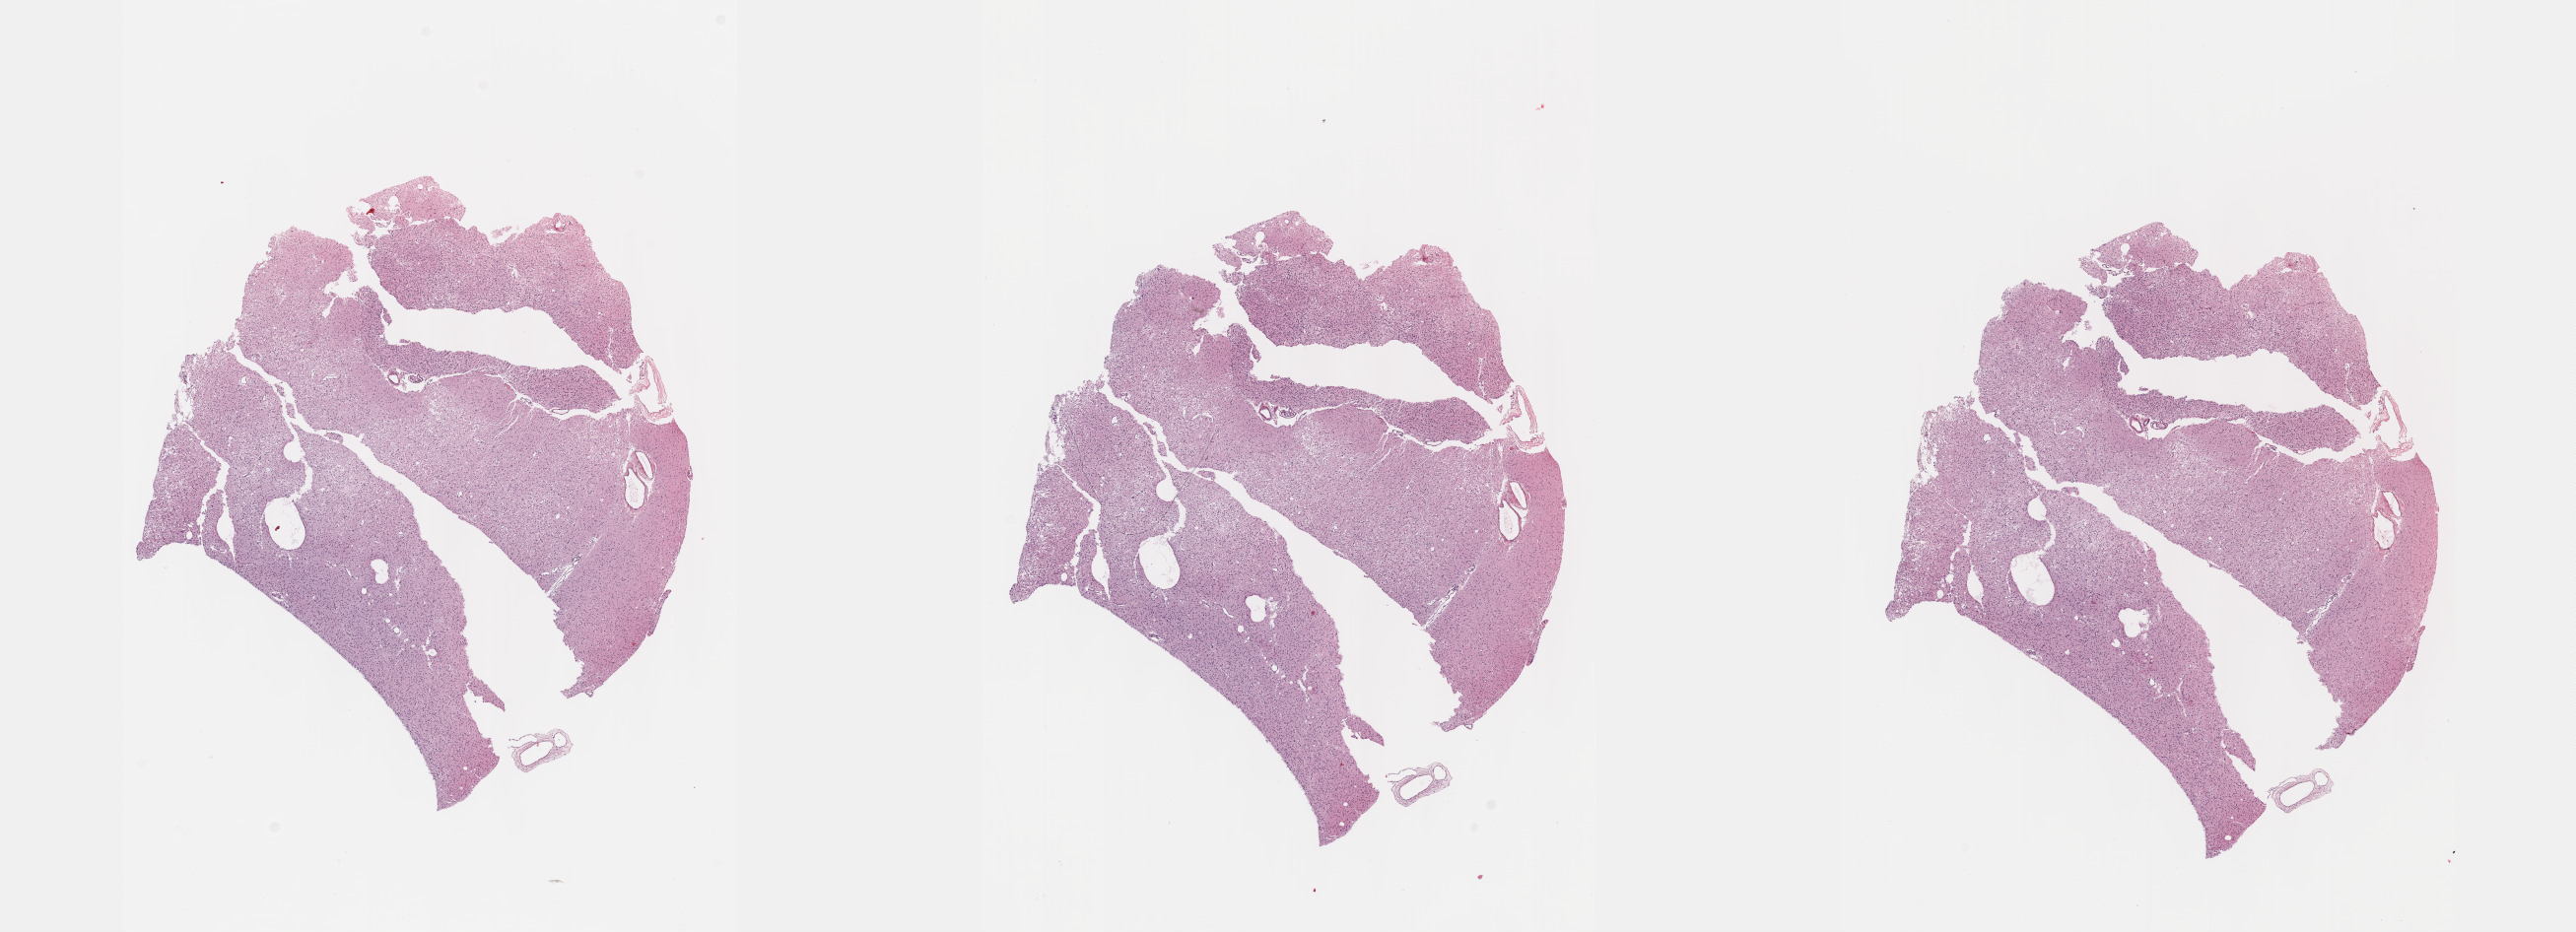
Hematoxylin and eosin (H&E) stained whole-slide image, a low-resolution overview of the entire scanned area, about 21.1 x 7.6 mm, formalin-fixed paraffin-embedded (FFPE) diagnostic section, brain, primary tumour sample. Female, age 53 years at initial diagnosis. Histologic grade: G2 (moderately differentiated).
- diagnosis: Oligodendroglioma, NOS (cerebrum)